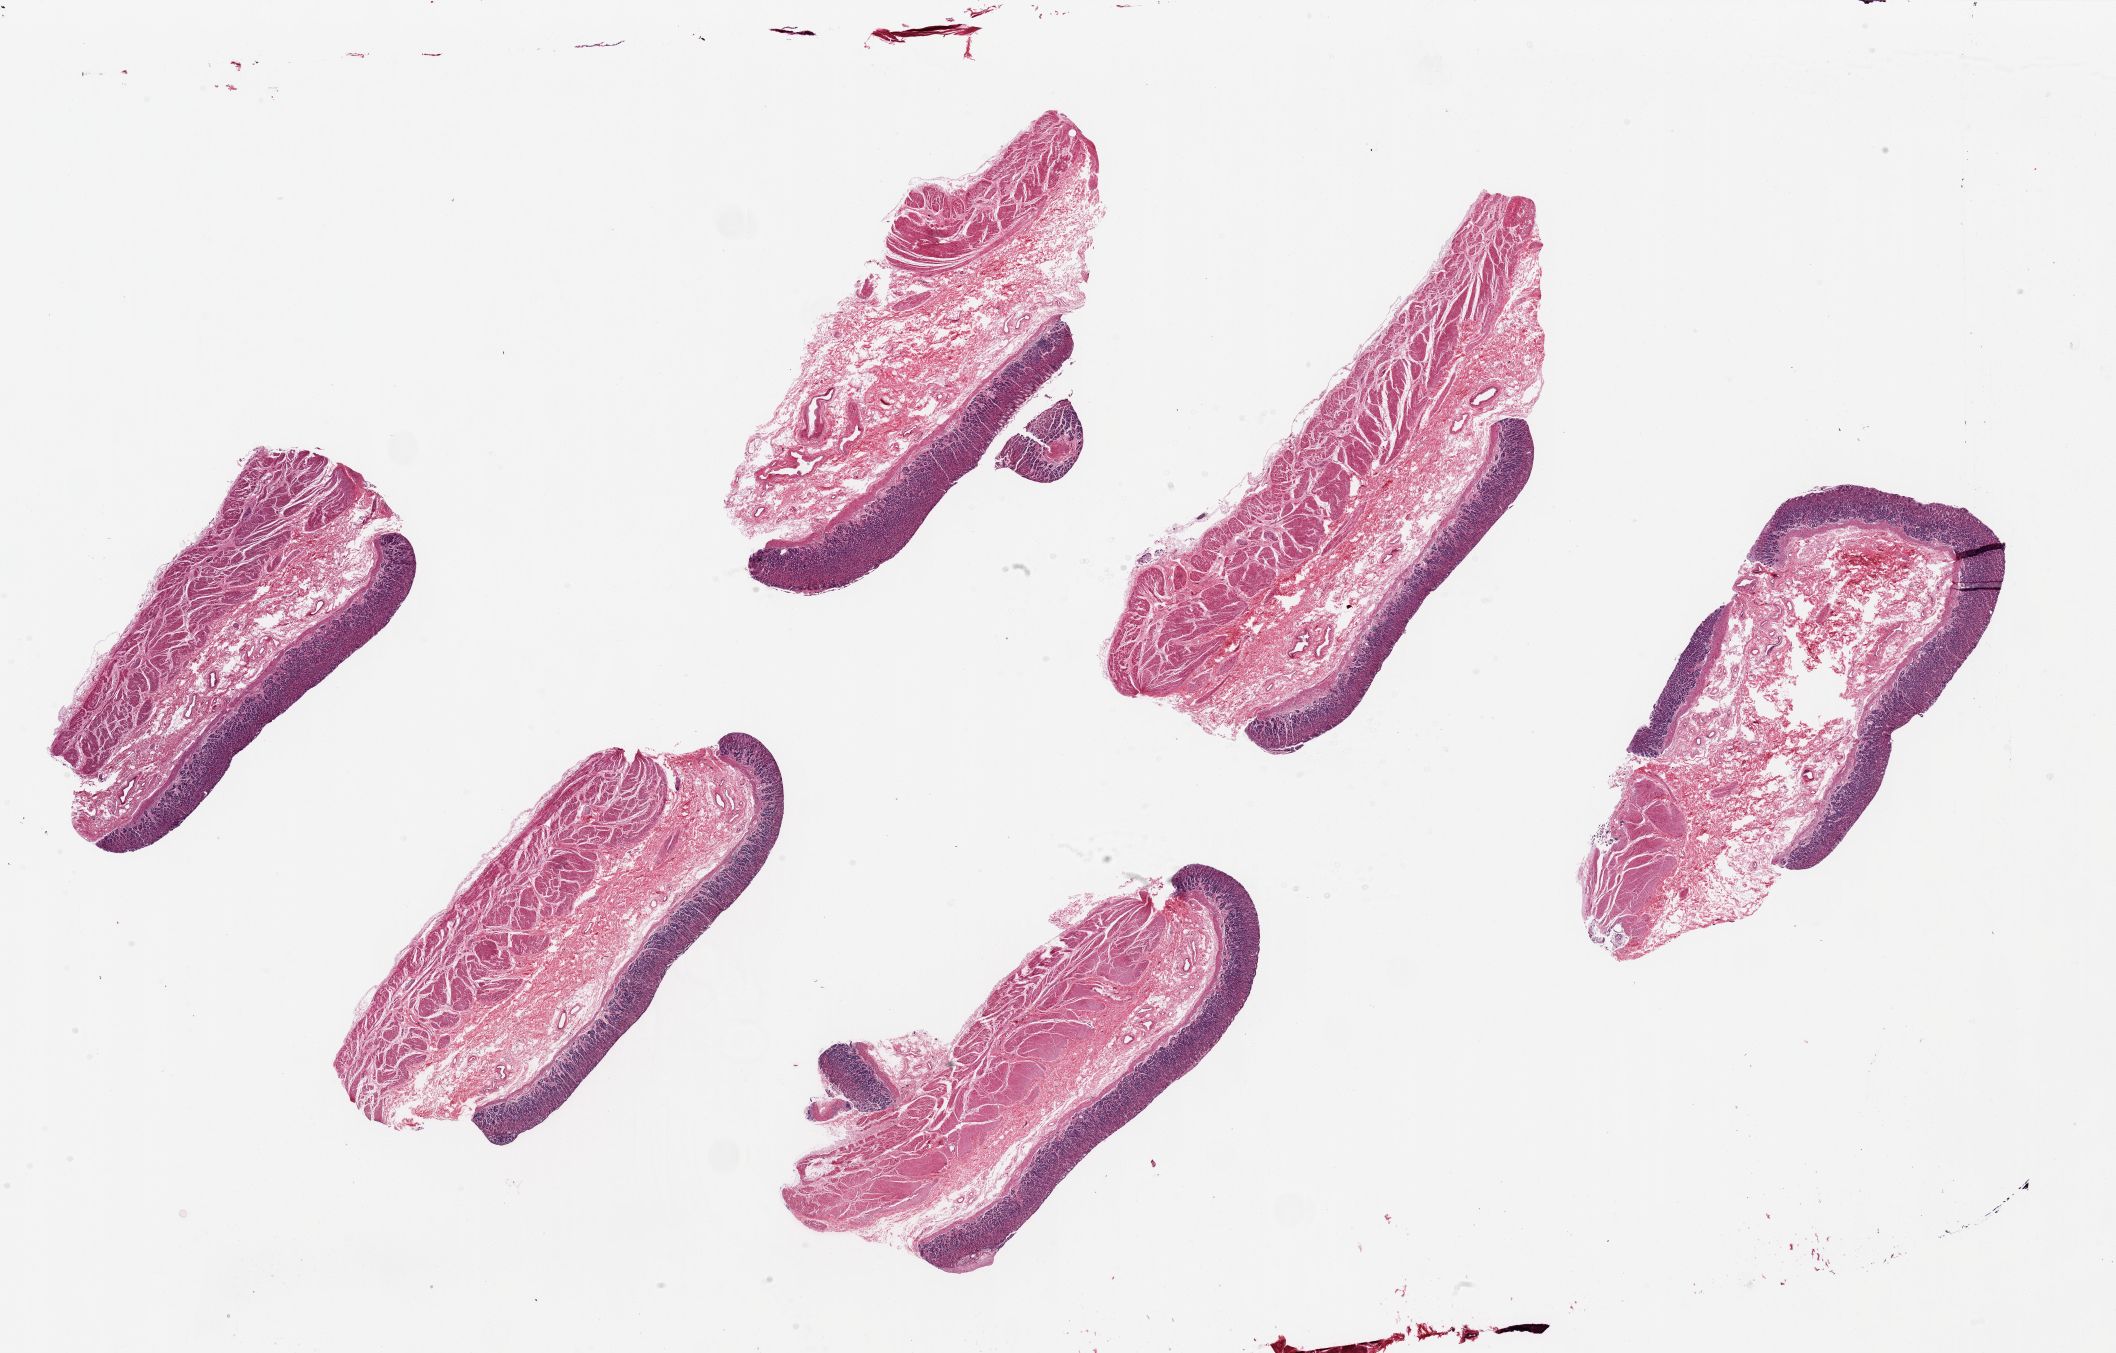
Haematoxylin and eosin whole-slide image — a low-resolution overview of the entire scanned area, about 33.5 x 21.4 mm (slide scanned at 20x). PAXgene-fixed, paraffin-embedded tissue. Sampled site (target tissue): stomach. Donor tissue sample. Donor: female.
Review note (as recorded): 6 pieces, ~8.5x3mm. Mucosa remarkably well preserved, ~20-25% of thickness.